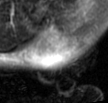
MRI of an extremity soft-tissue mass, one axial slice; position 29 of 42 along the scan axis; T2-weighted fat-saturated; MR volume resampled by the dataset authors to the PET/CT grid (not the native acquisition matrix); 3.27 mm slice thickness; 108 × 103 image matrix. Male patient. From the clinical record (not read from this slice): histological type: leiomyosarcoma; grade: intermediate; site of the primary tumour: left pelvis.
Outlined on this slice (expert contour drawn on MRI and transferred to this co-registered scan by the dataset authors):
- gross tumour volume (mass): bounding box <25,21,83,70> (left, top, right, bottom; pixels)